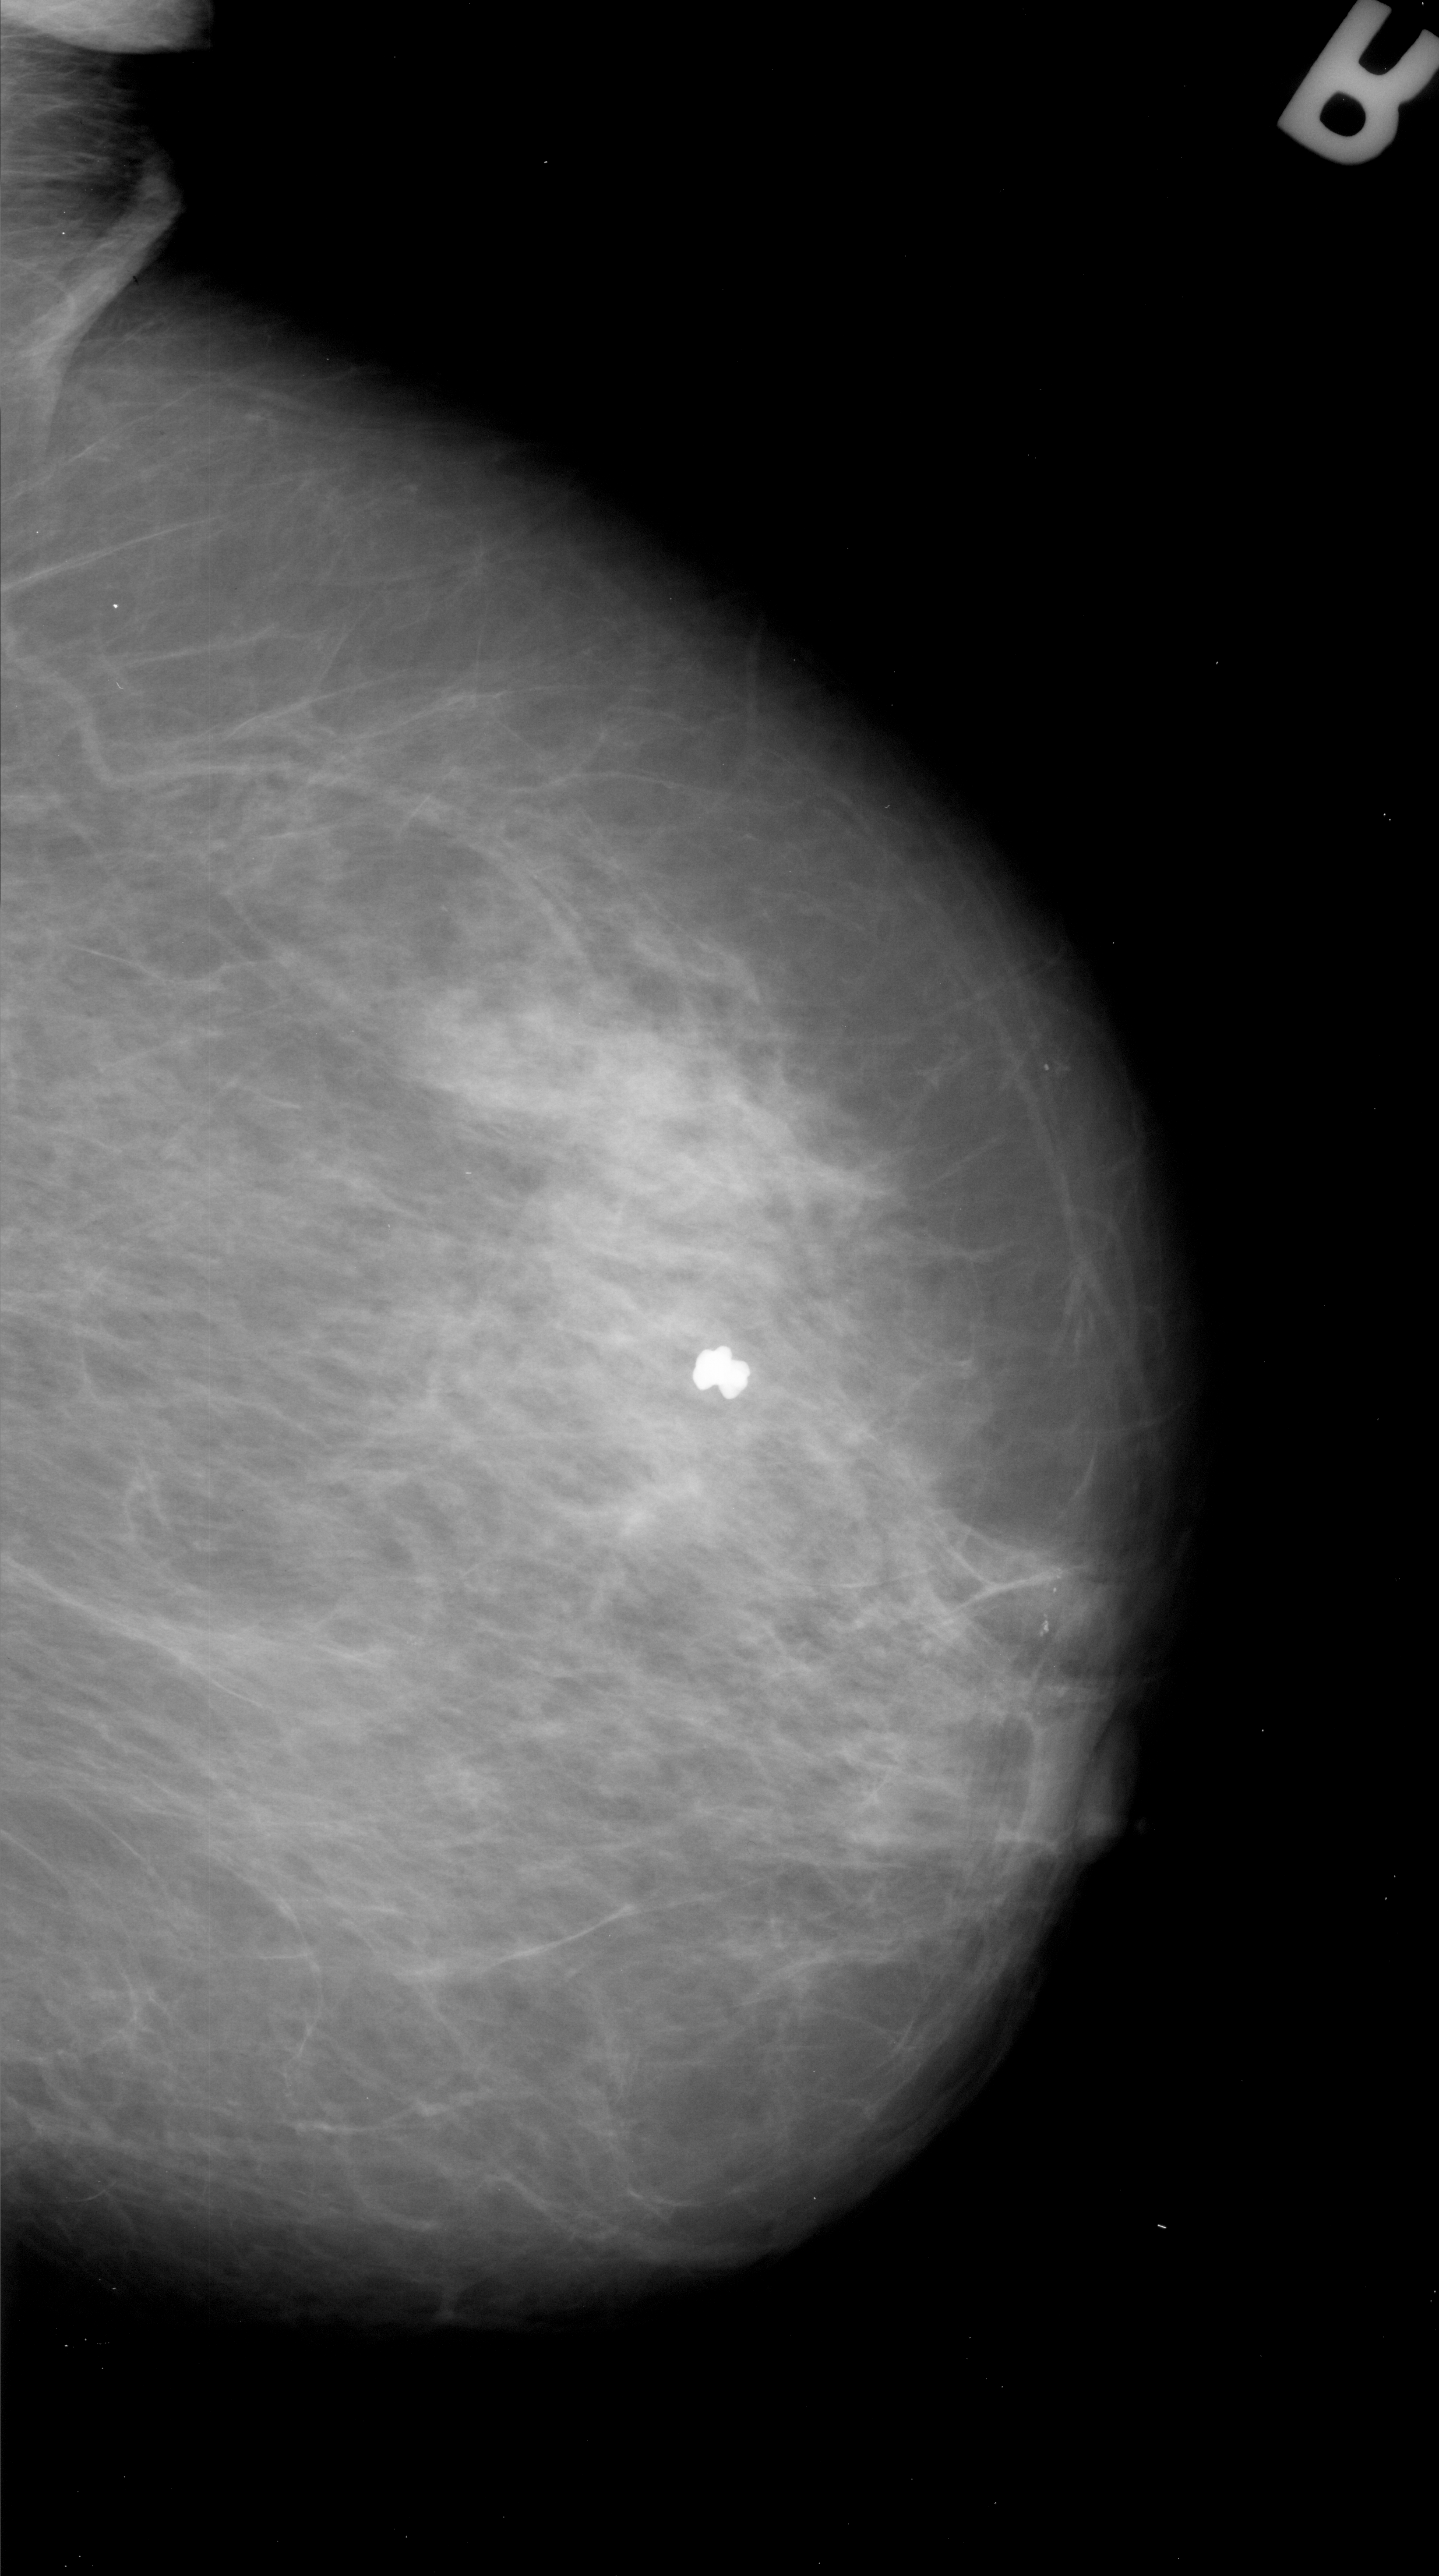
Digitized screen-film mammogram. Right breast. Mediolateral oblique (MLO) view. Breast composition: heterogeneously dense (BI-RADS density category 3 of 4). 1439 × 2576 image matrix.
Expert-marked regions of interest on this image (one box per marked abnormality):
- calcifications, morphology pleomorphic, distribution linear; BI-RADS assessment category 4; pathology (as recorded): malignant: box from (x=1025, y=1555) to (x=1079, y=1649) px